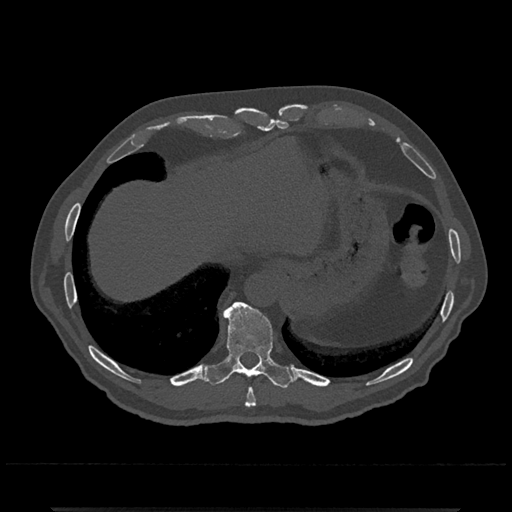
CT including the spine, one axial slice; slice 564 of 797 in the series (ordered by position); reconstruction kernel Br40s/3; 120 kVp; bone window (W 1800 / L 400 HU); 0.5 mm slice thickness; 512 × 512 image matrix. Patient: male, 67 years. Case-level facts recorded for this patient, not image findings: primary cancer: prostate.
Structures marked on this image (semi-automatic segmentation, software-assisted and operator-edited):
- T10 vertebra: bounding box (x1, y1, x2, y2) in pixels: (203, 301, 293, 389)
- T9 vertebra: (245, 388, 256, 407)